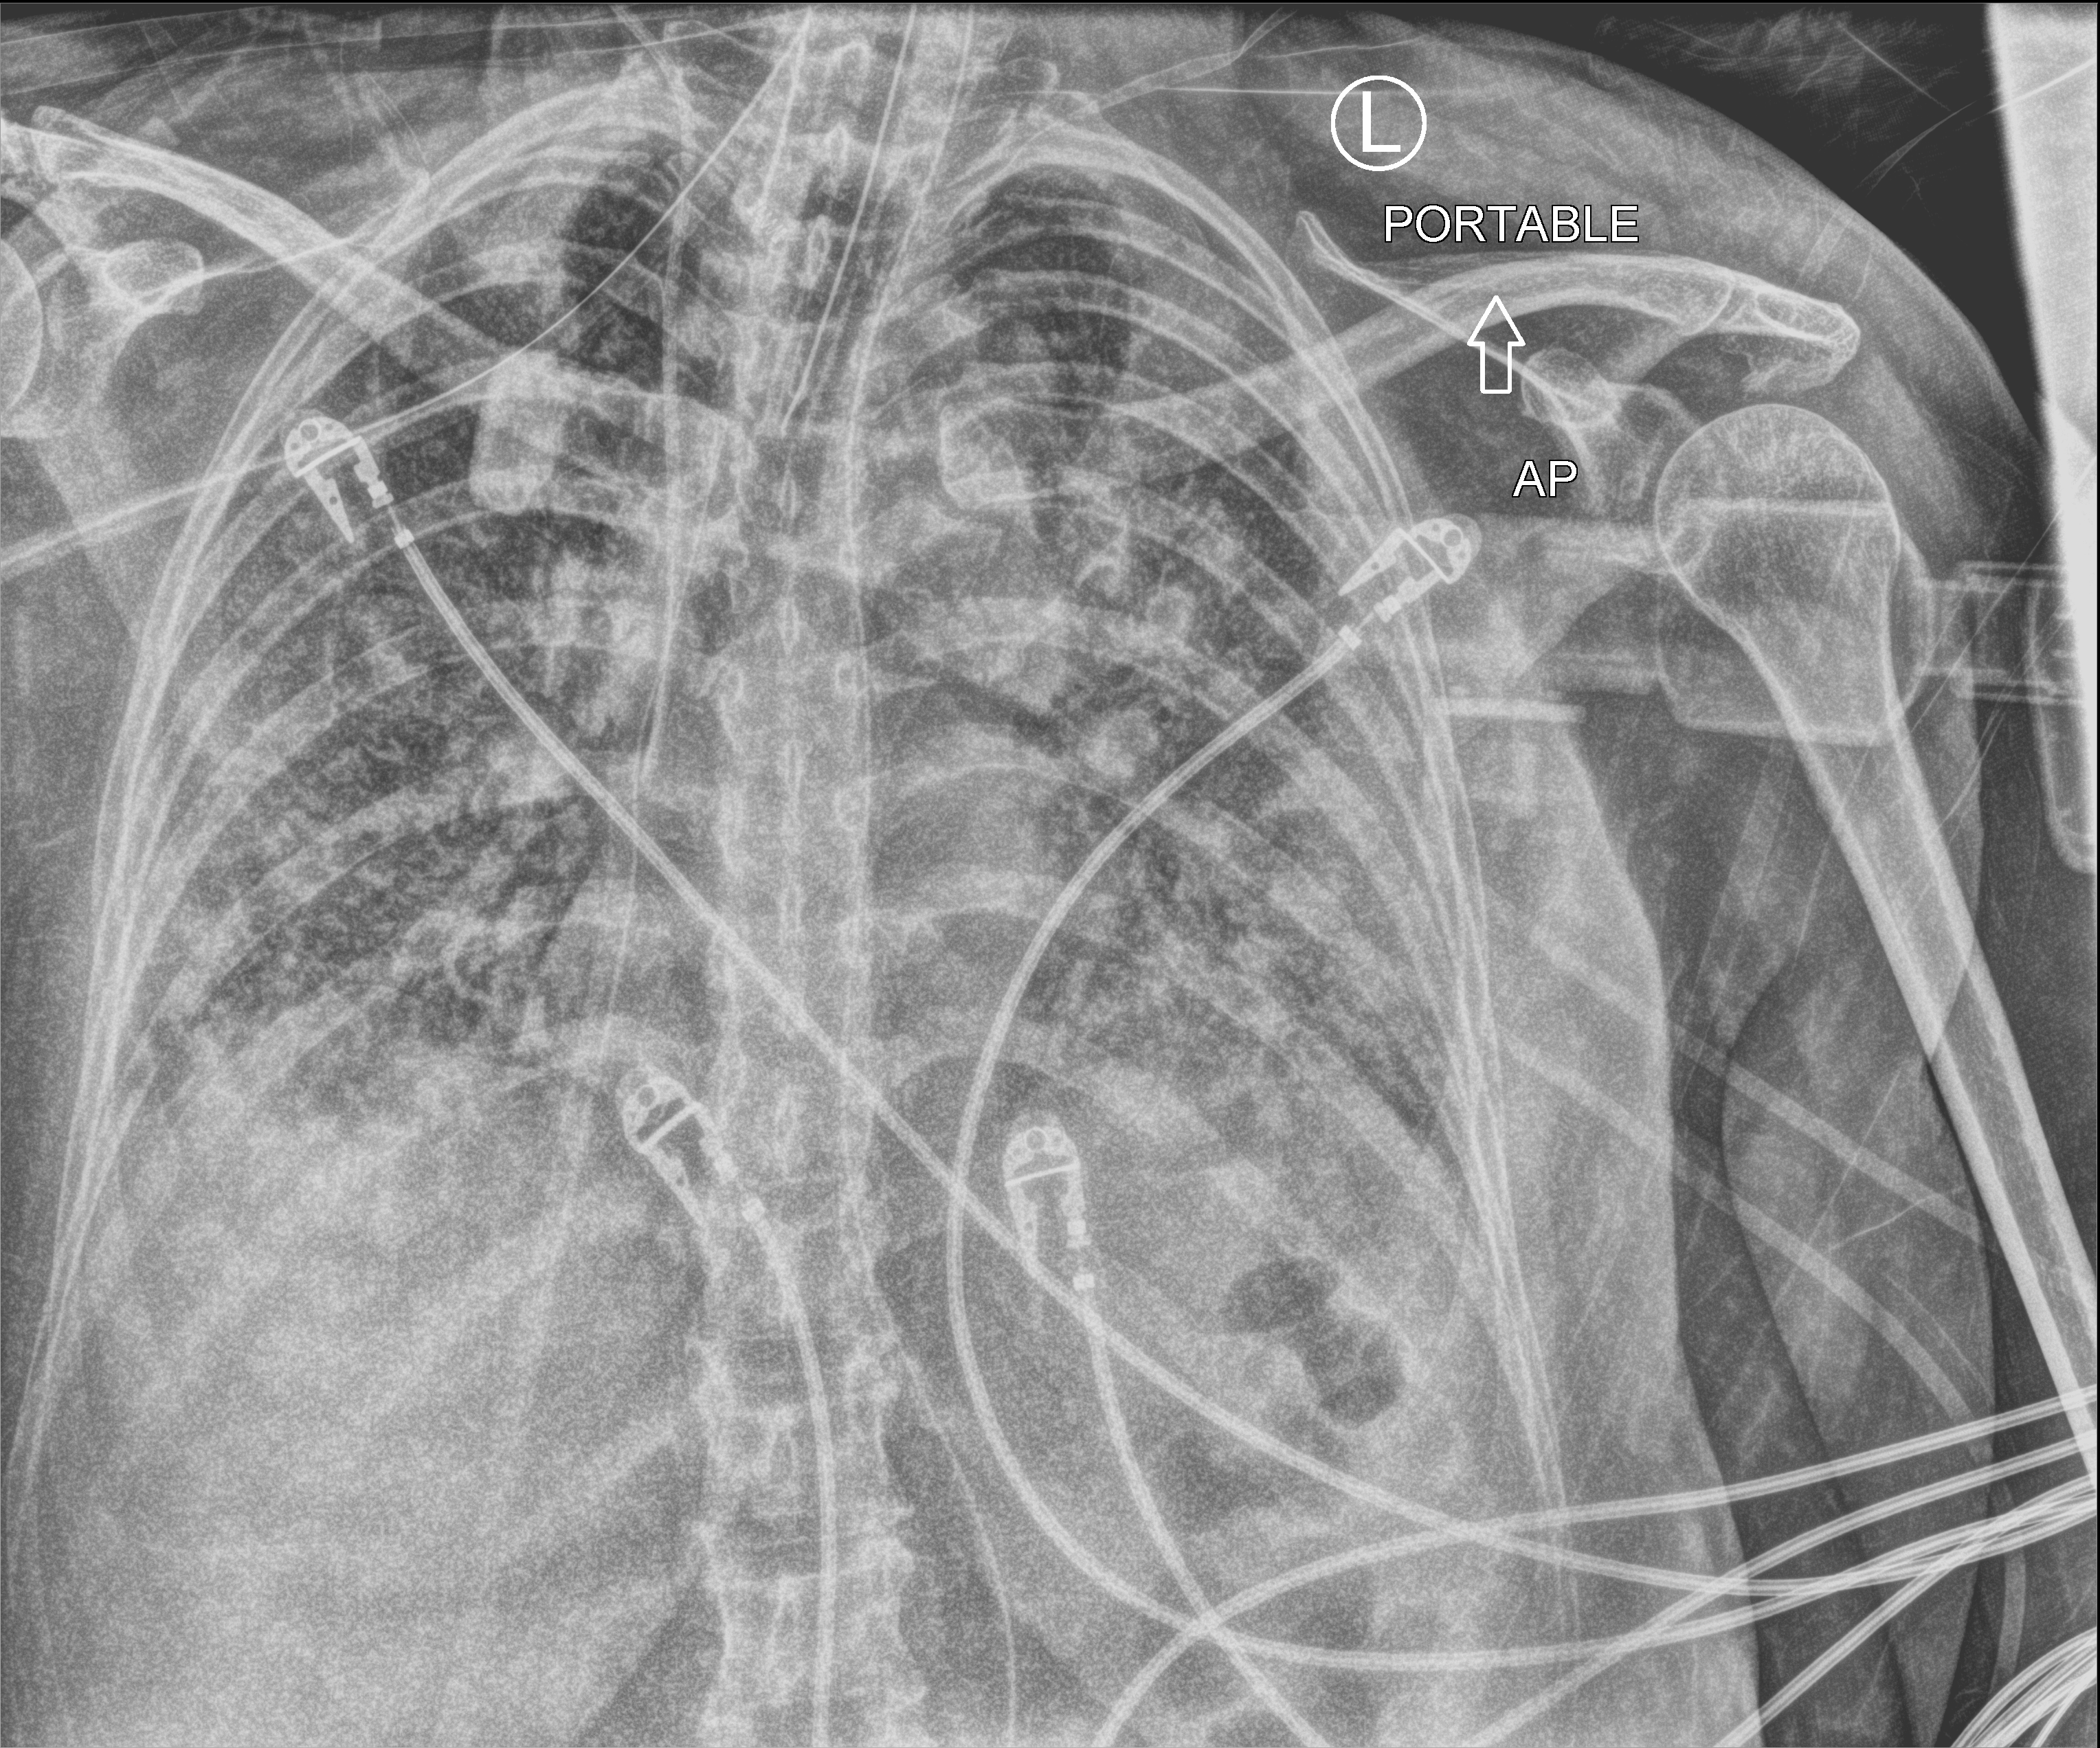
Bedside chest radiograph (computed radiography). Patient hospitalised with COVID-19; female, aged 60–74 years.
Hospital-stay facts (about this admission, not read from this image; timing relative to this image not recorded): length of hospital stay: 43 days.